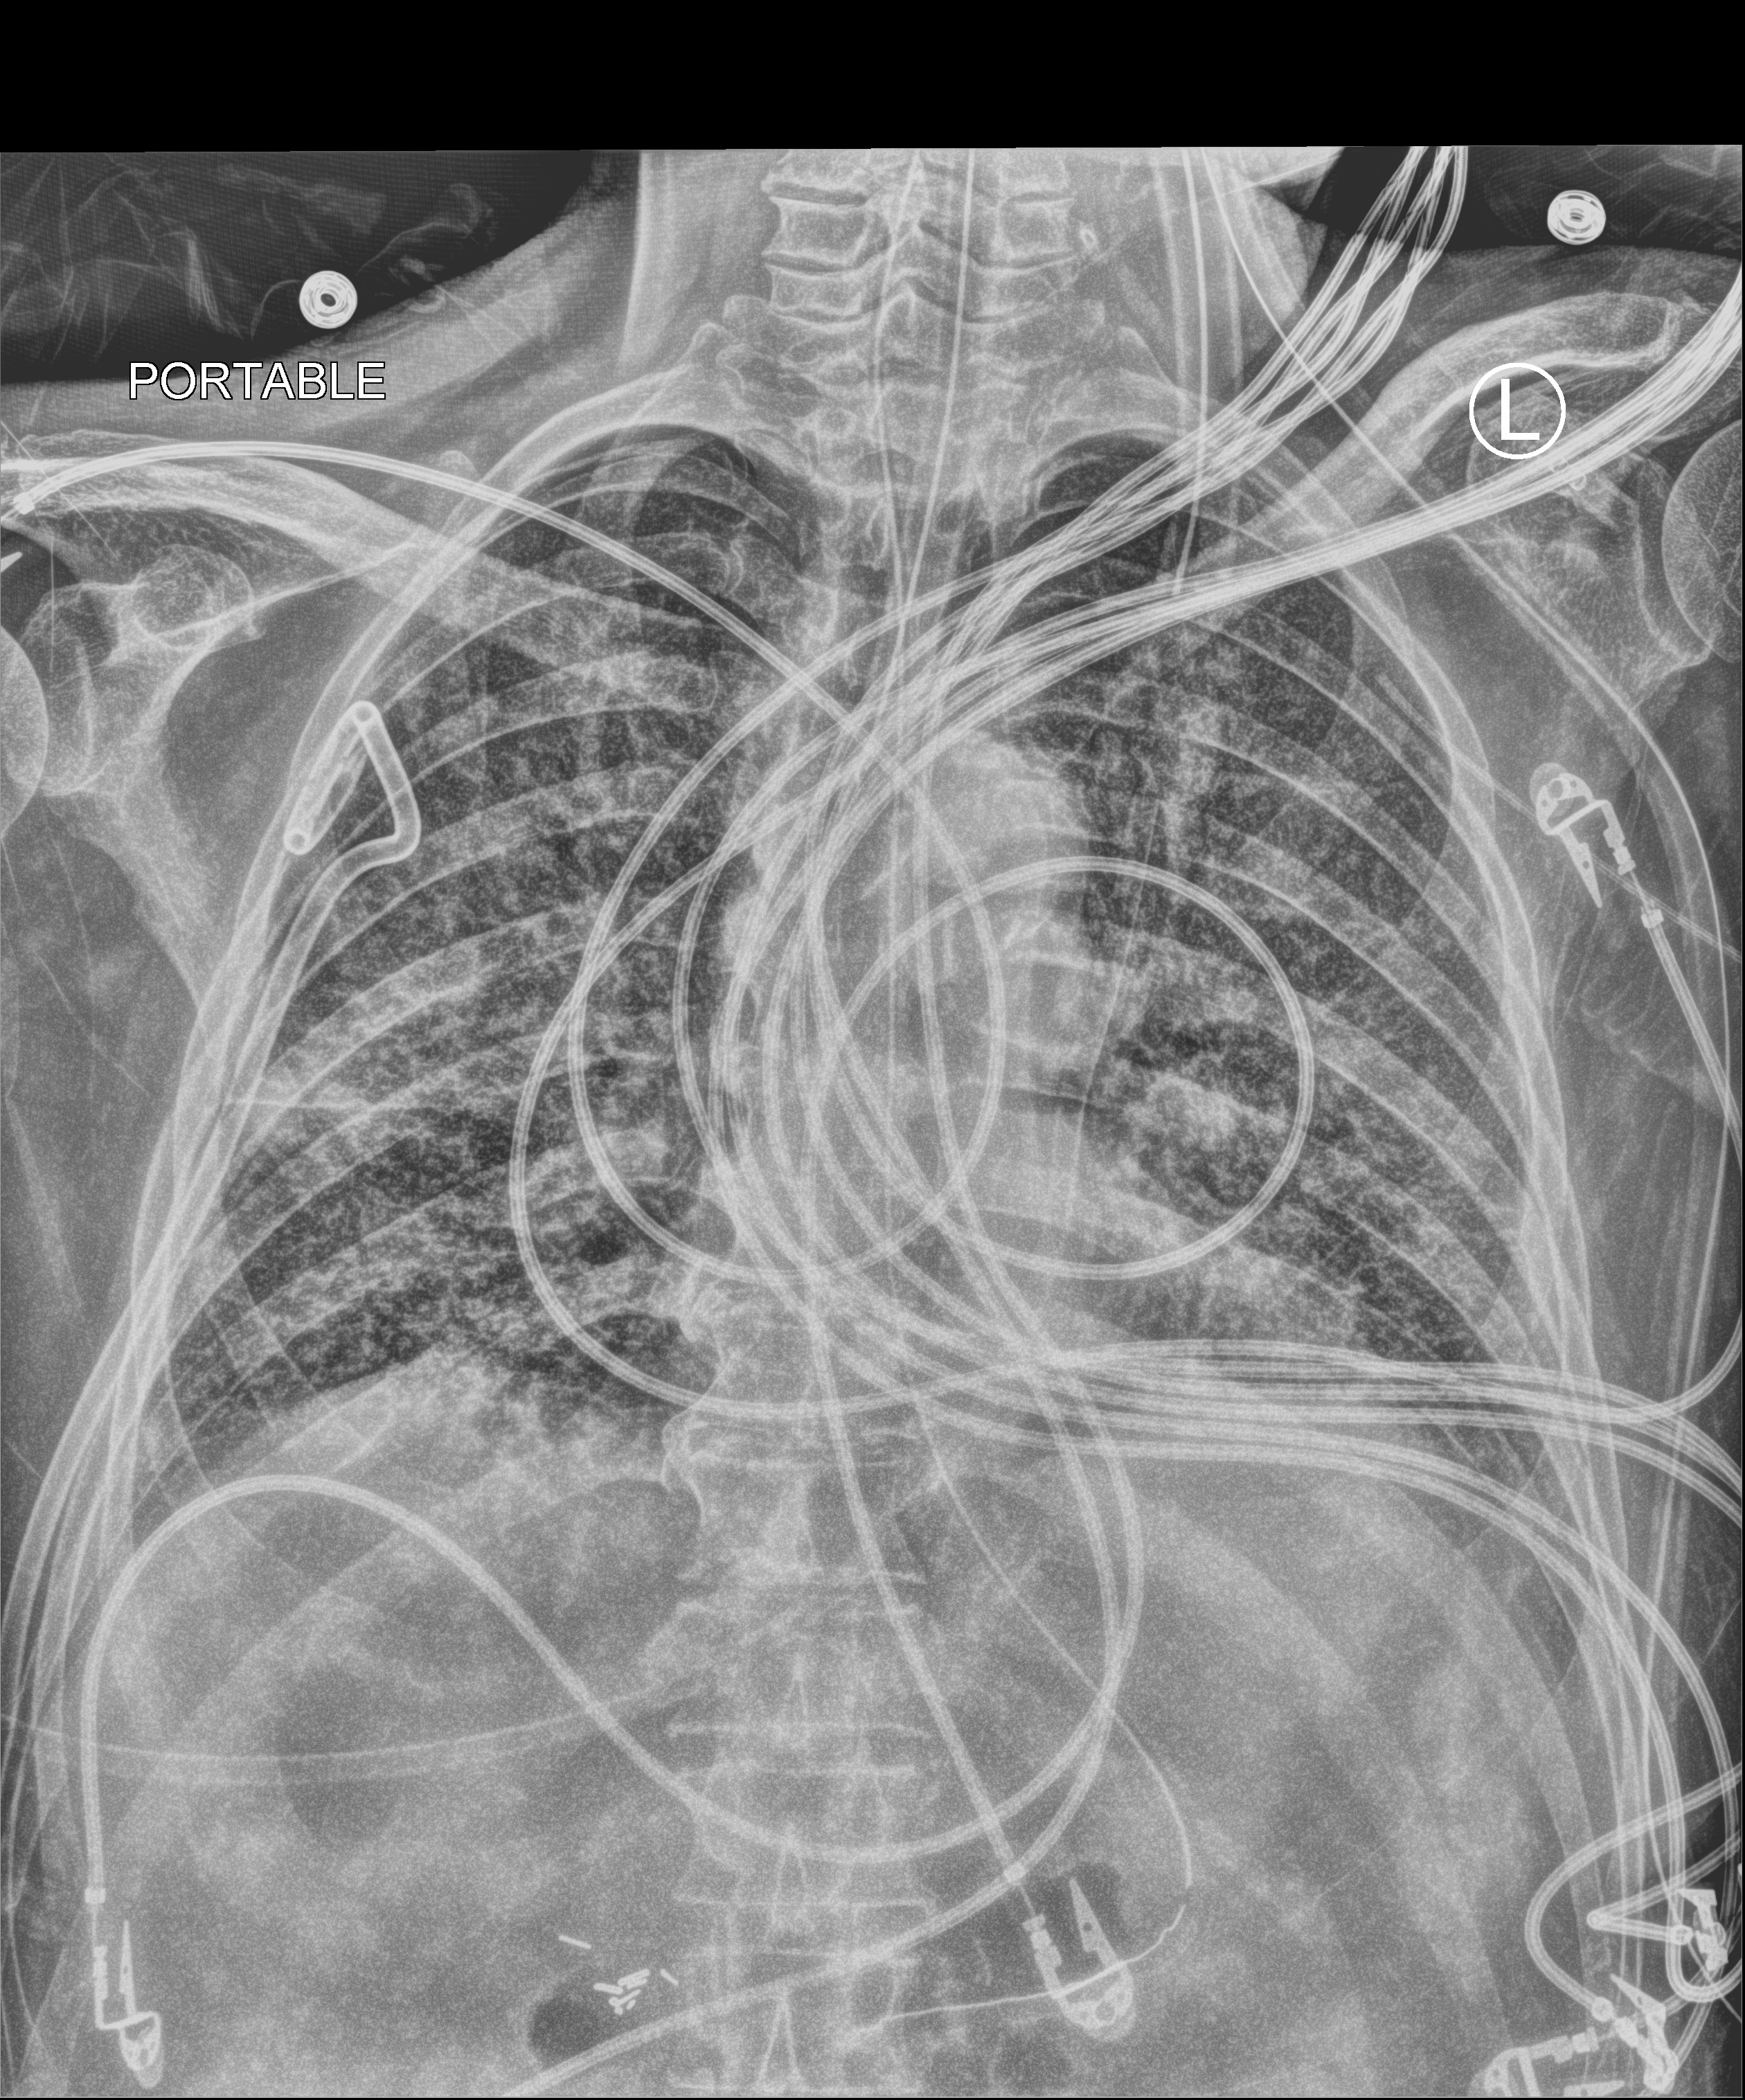
Bedside chest radiograph (computed radiography), anteroposterior (AP) projection. Patient hospitalised with COVID-19; male, aged 75–90 years.
Hospital-stay facts (about this admission, not read from this image; timing relative to this image not recorded):
- admitted to intensive care during this hospital stay: yes
- mechanically ventilated during this hospital stay: yes
- diabetes (admission record): no